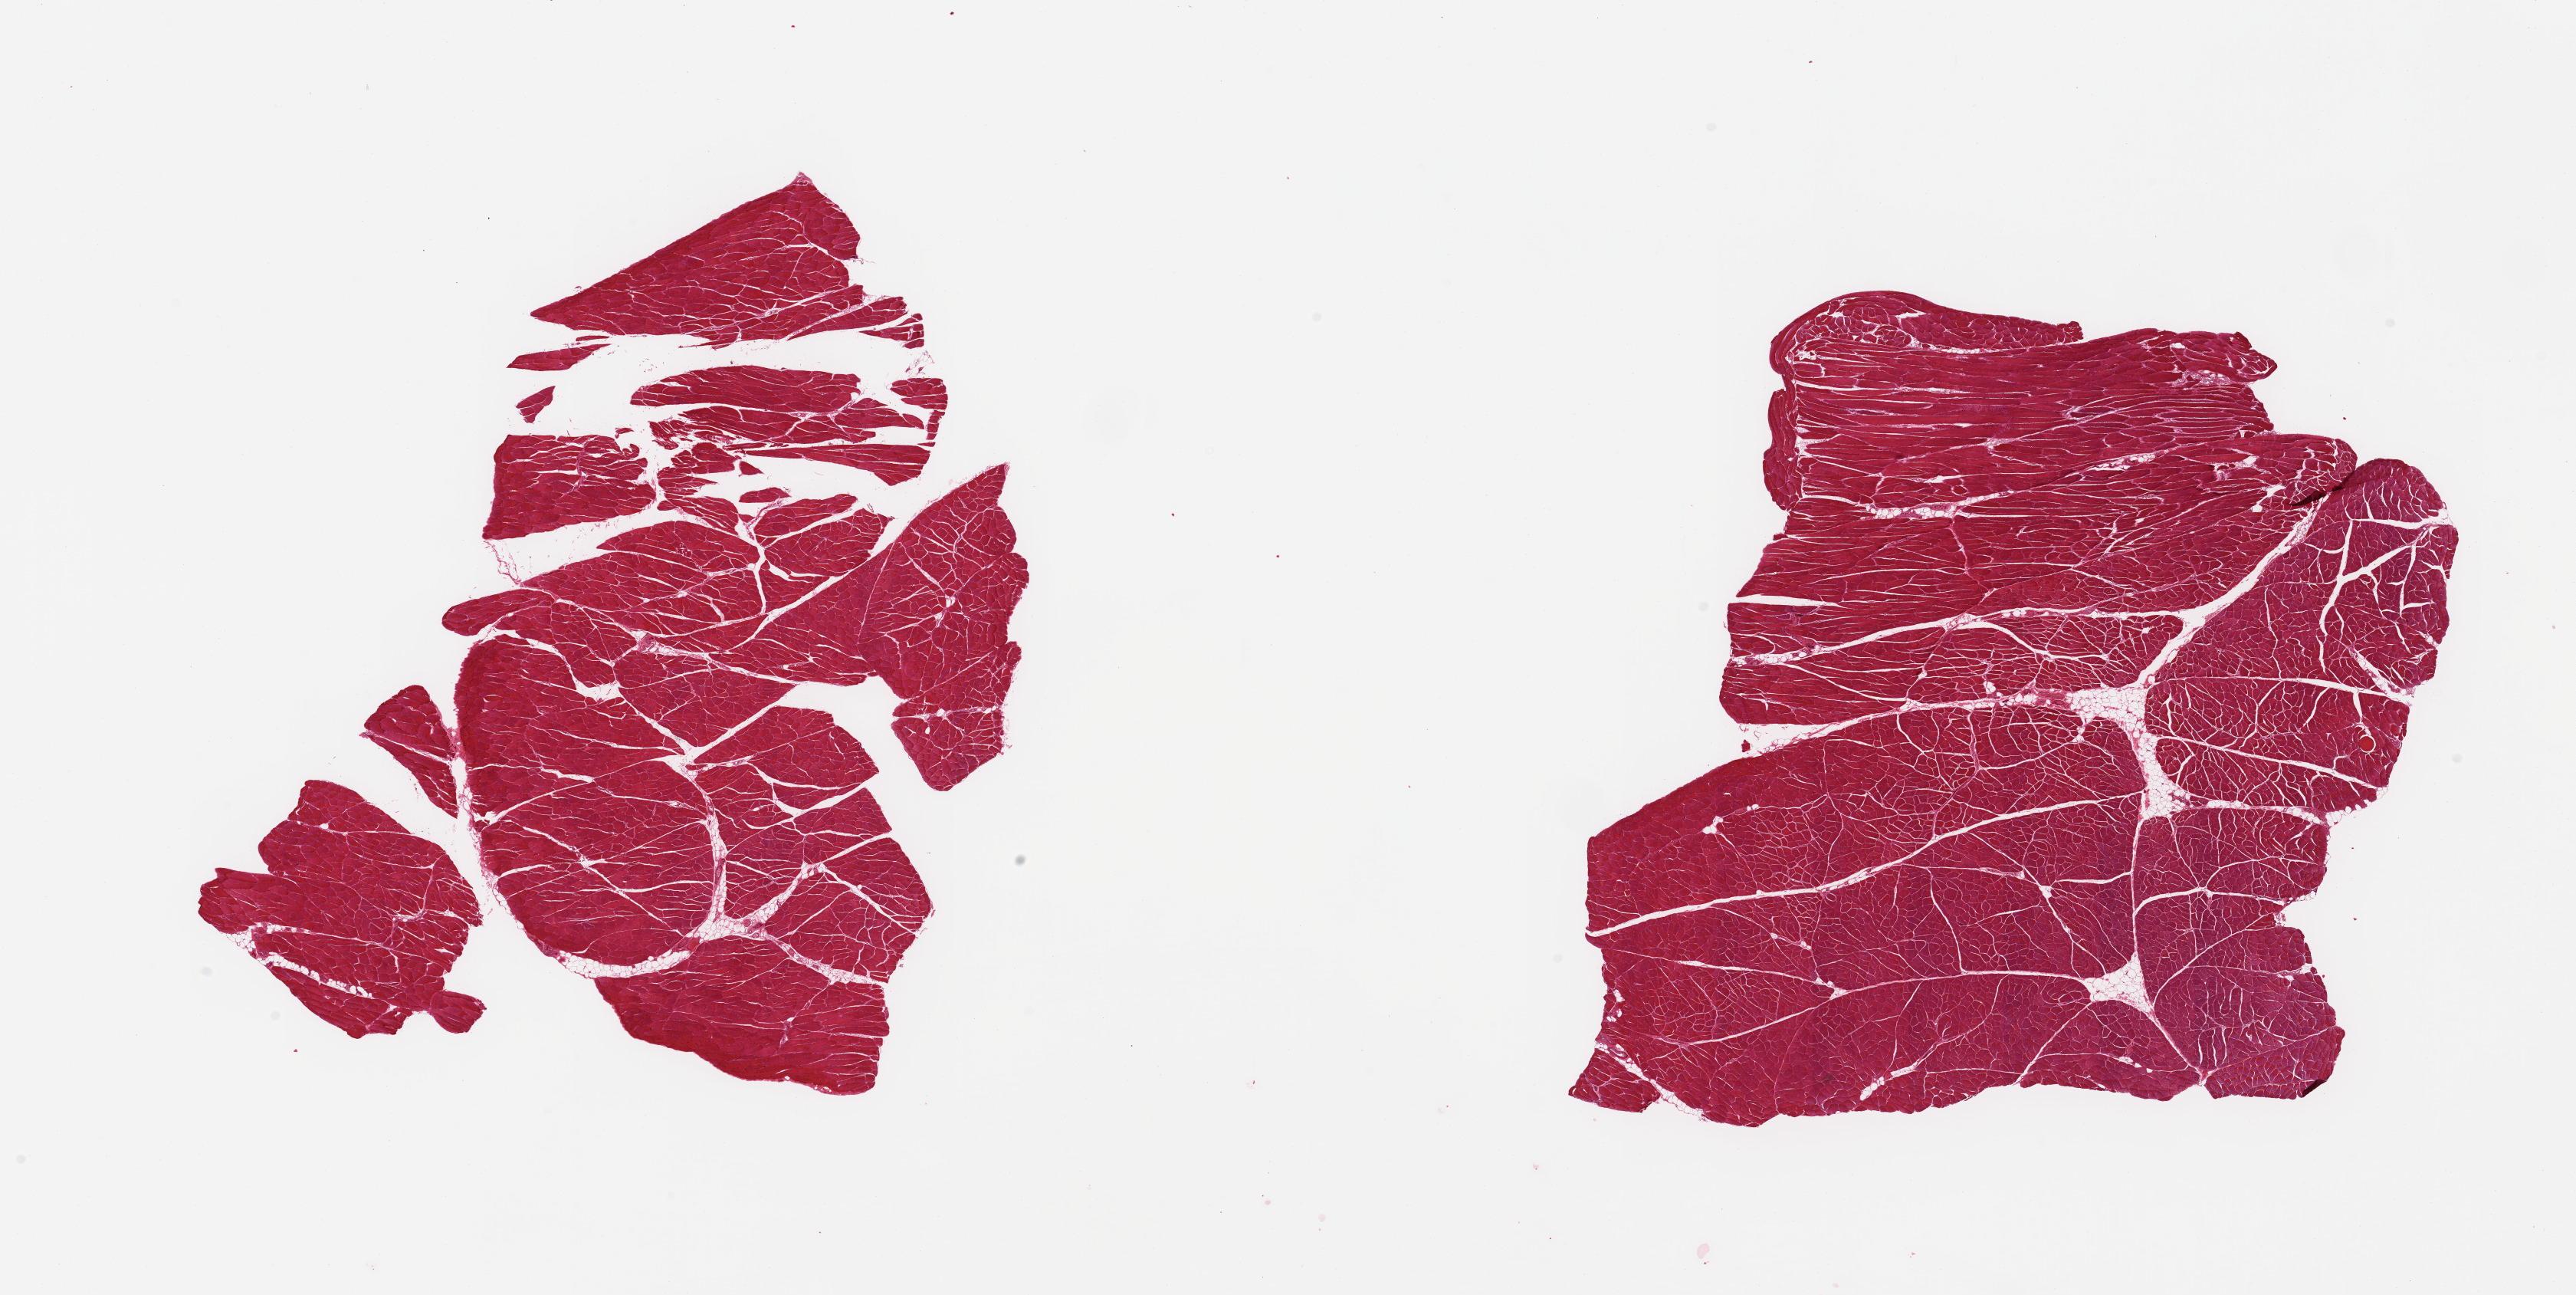
Haematoxylin and eosin whole-slide image — shown as a low-resolution overview of the whole scanned area (about 26.6 x 13.4 mm), PAXgene-fixed paraffin-embedded (PFPE) section, target tissue: skeletal muscle, donor tissue sample. Donor: male.
• review note (as recorded): 2 pieces; skeletal muscle with minimal internal fat